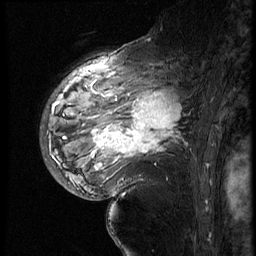
Breast MRI (dynamic contrast-enhanced), one sagittal slice; slice 41 of 60 in the series (ordered by position); 4 images stored at this slice position (order not interpretable as contrast timing); 1.5 T; TE 4.2 ms, TR 9 ms; 256 × 256 image matrix. Female patient, age 56 years. Case-level facts recorded for this patient, not image findings: setting: breast cancer imaged before/during neoadjuvant chemotherapy; receptor status: HER2-positive.
Annotated regions visible in this slice (semi-automatically segmented with operator editing):
- analysis volume of interest (the breast-tissue region the enhancement analysis was run in; not a lesion): box from (x=82, y=83) to (x=199, y=177) px
- tumour enhancement mask (voxels above the 140 % enhancement threshold inside the analysis volume of interest): (x=92, y=93)–(x=182, y=167)